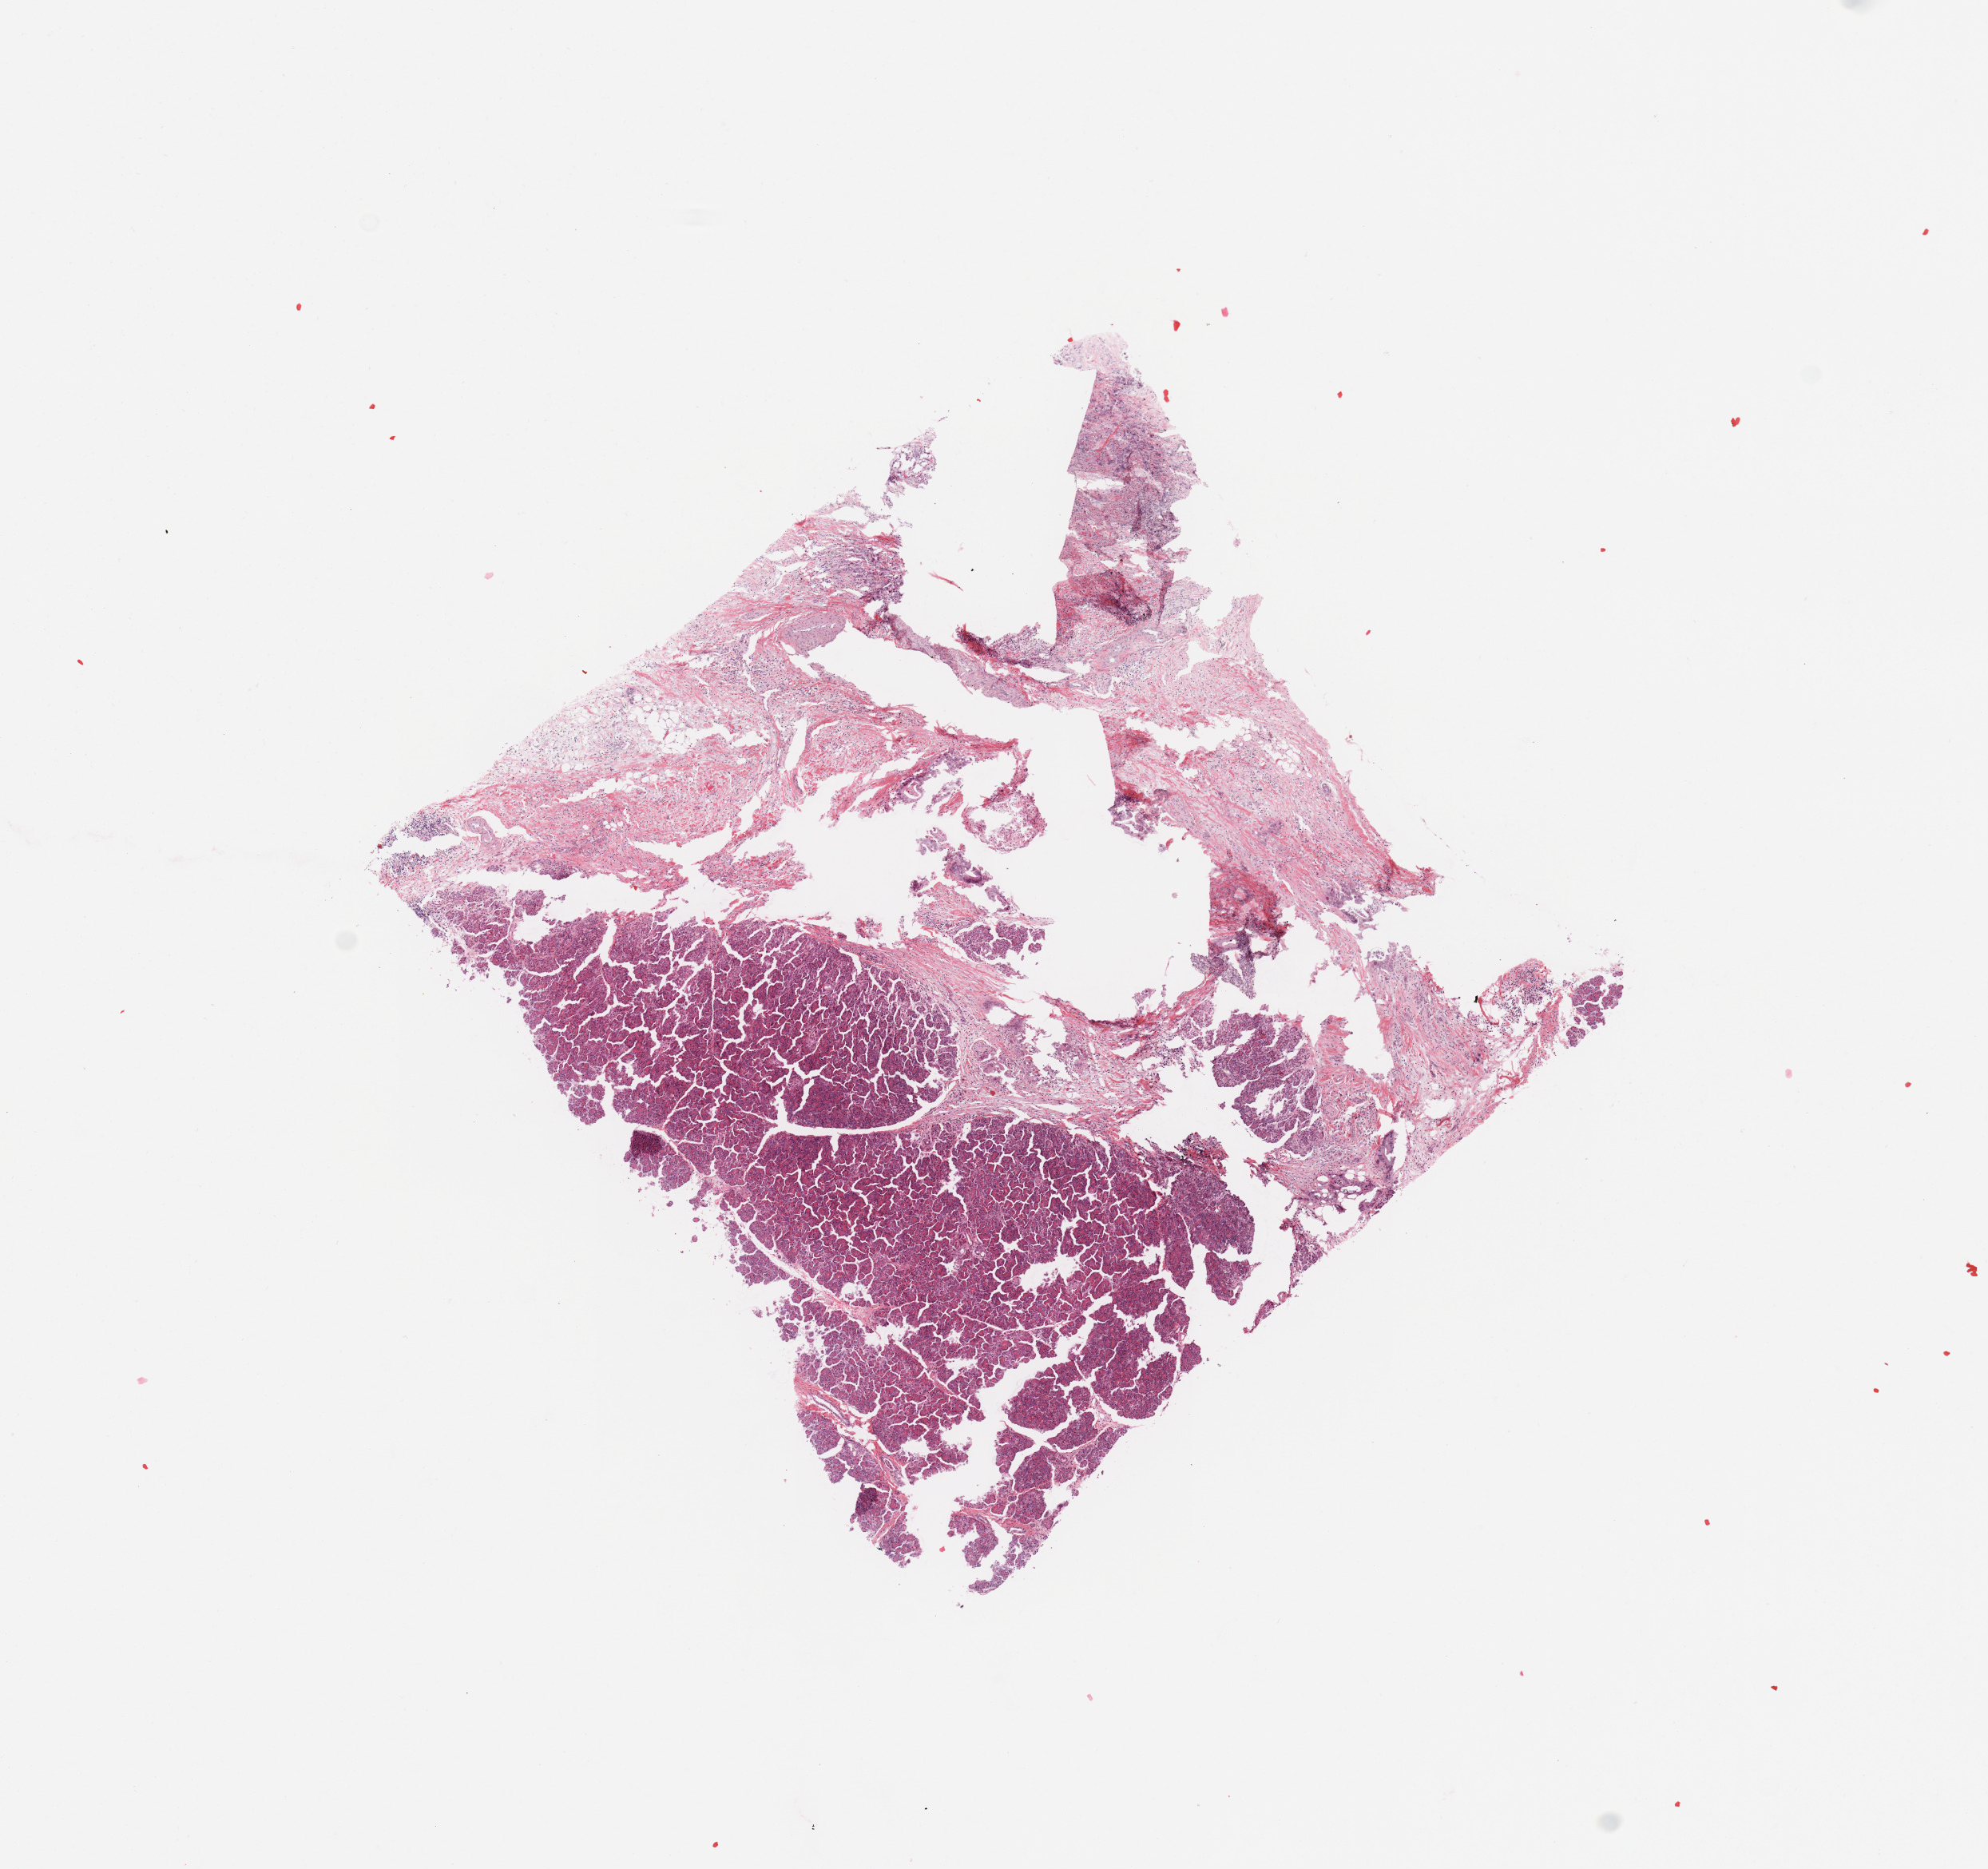
H&E-stained whole-slide image — low-resolution overview of the scanned area, about 9.8 x 9.3 mm (slide scanned at 20x), pancreas, tumour tissue. Female, 64 y/o. Histologic grade: G2 (moderately differentiated).
Primary tumour site (as recorded): head. Histologic diagnosis: Infiltrating duct carcinoma, NOS. AJCC pathologic stage: III.